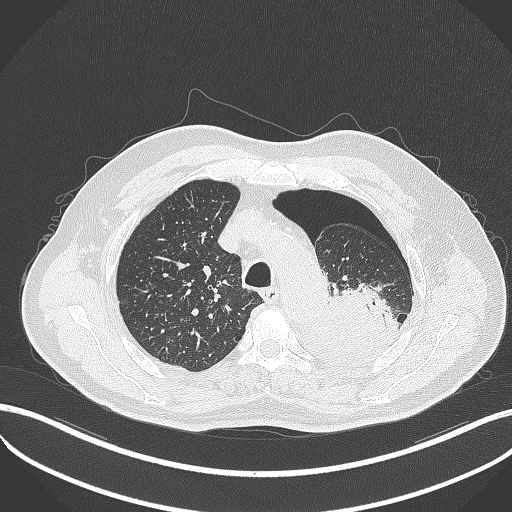
Chest CT, one axial slice; slice 390 of 464 in the series (ordered by position); reconstruction kernel B70f; 120 kVp; lung window (W 1500 / L -600 HU); 1 mm slice thickness; 512 × 512 image matrix, field of view 400 × 400 mm. Patient: male, 76 years. From the clinical record (not read from this slice): clinical TNM (as recorded): T3 N0 M1b.
Outlined on this slice (bounding box drawn by a radiologist):
- lung tumour (recorded histology: adenocarcinoma): bounding box (x1, y1, x2, y2) in pixels: (312, 285, 401, 368)